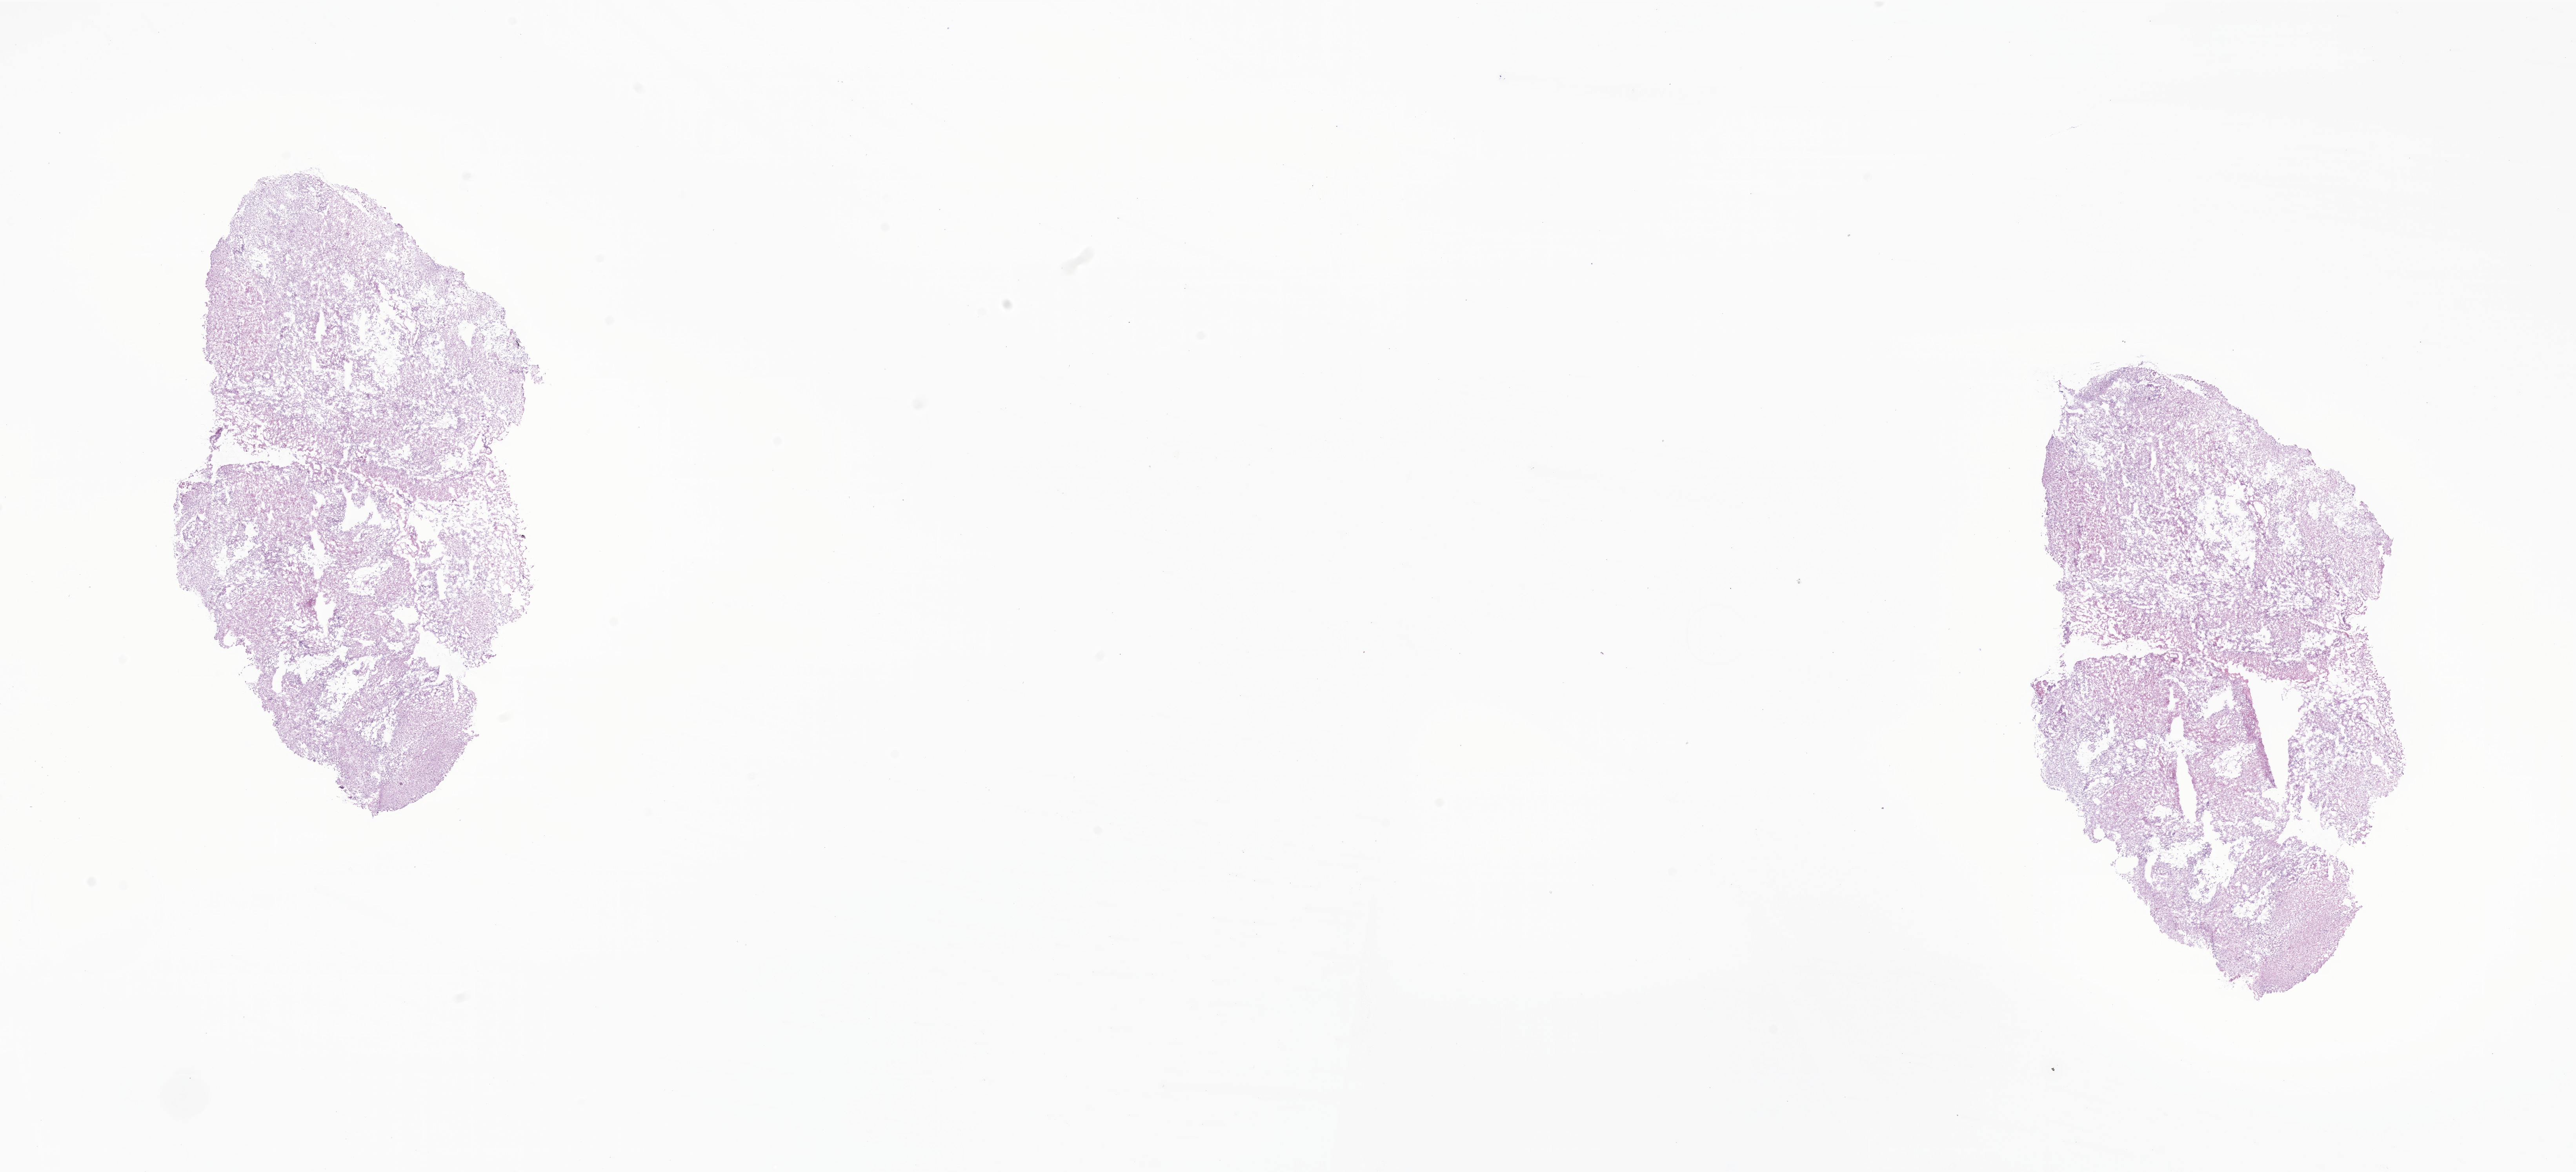
Whole-slide image, haematoxylin and eosin stain of tumor tissue from the cerebellum — whole scanned area (about 27.7 x 12.6 mm) shown as a low-resolution overview, frozen section. Patient female; age 69 months (5 years 9 months).
Diagnosis: Pilocytic astrocytoma.